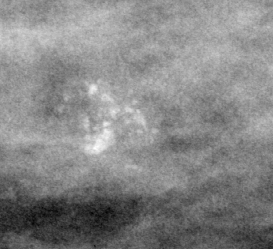
Crop from a digitized film mammogram around one marked abnormality; left breast; CC view; BI-RADS breast density category 2 (scale 1–4).
- Finding: calcifications, morphology pleomorphic / fine linear branching, distribution regional; BI-RADS assessment category 5; pathology result (as recorded, not read from the image): malignant.